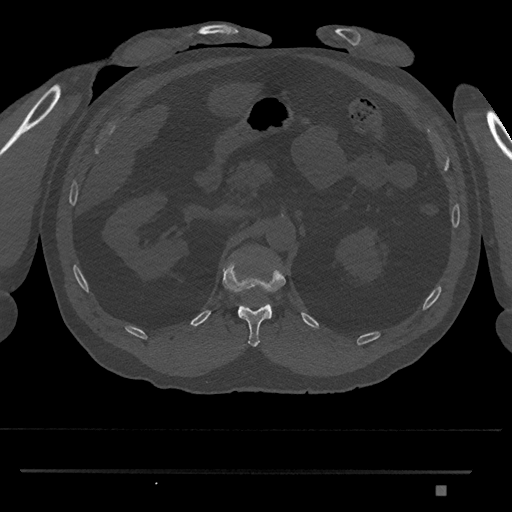
CT including the spine, one axial slice. Position 869 of 1134 along the scan axis. Reconstruction kernel Br40s/3. Bone window (W 1800 / L 400 HU). 512 × 512 image matrix. Male patient, age 65 years. Case-level facts recorded for this patient, not image findings: primary cancer: prostate.
Structures marked on this image (semi-automatically segmented with operator editing):
- L1 vertebra: box from (x=270, y=305) to (x=273, y=317) px
- T12 vertebra: (x=222, y=260)–(x=286, y=347)